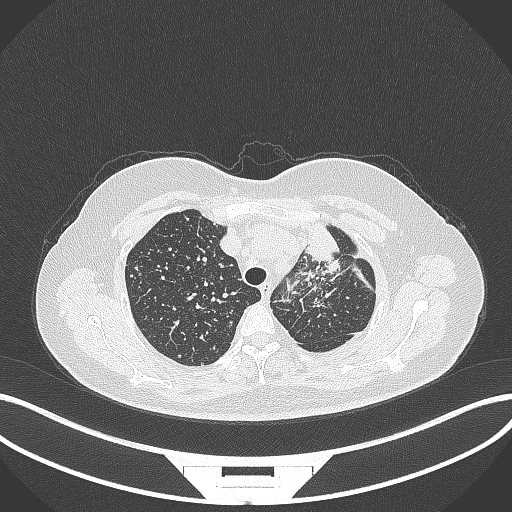
Chest CT, one axial slice; position 266 of 348 along the scan axis; lung window (W 1500 / L -600 HU); 1 mm slice thickness; 512 × 512 image matrix. Female patient, age 49 years. Case-level facts recorded for this patient, not image findings: clinical TNM (as recorded): T1c N0 M1.
Structures marked on this image (rectangle marked by the reading radiologist):
- lung tumour (recorded histology: adenocarcinoma): bounding box <298,213,341,271> (left, top, right, bottom; pixels)